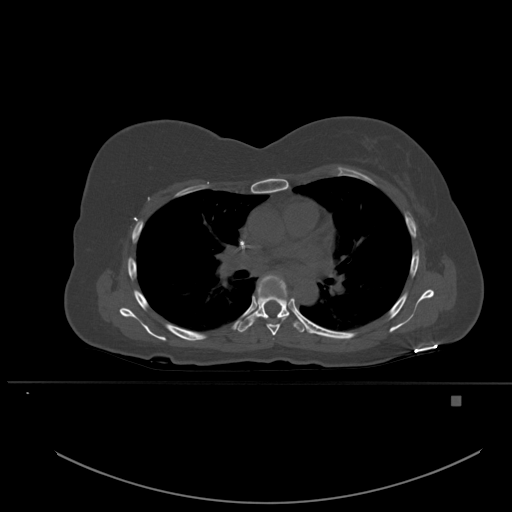
CT including the spine, one axial slice; position 357 of 651 along the scan axis; bone window (W 1800 / L 400 HU); 1.5 mm slice thickness; 512 × 512 image matrix, field of view 443 × 443 mm. Female patient, age 49 years. Case-level facts recorded for this patient, not image findings: primary cancer: breast; vertebrae with lytic lesions (as recorded): L3, T12, L4.
Annotated regions visible in this slice (semi-automatically segmented with operator editing):
- T5 vertebra: box from (x=264, y=316) to (x=287, y=336) px
- T6 vertebra: (x=238, y=274)–(x=305, y=333)